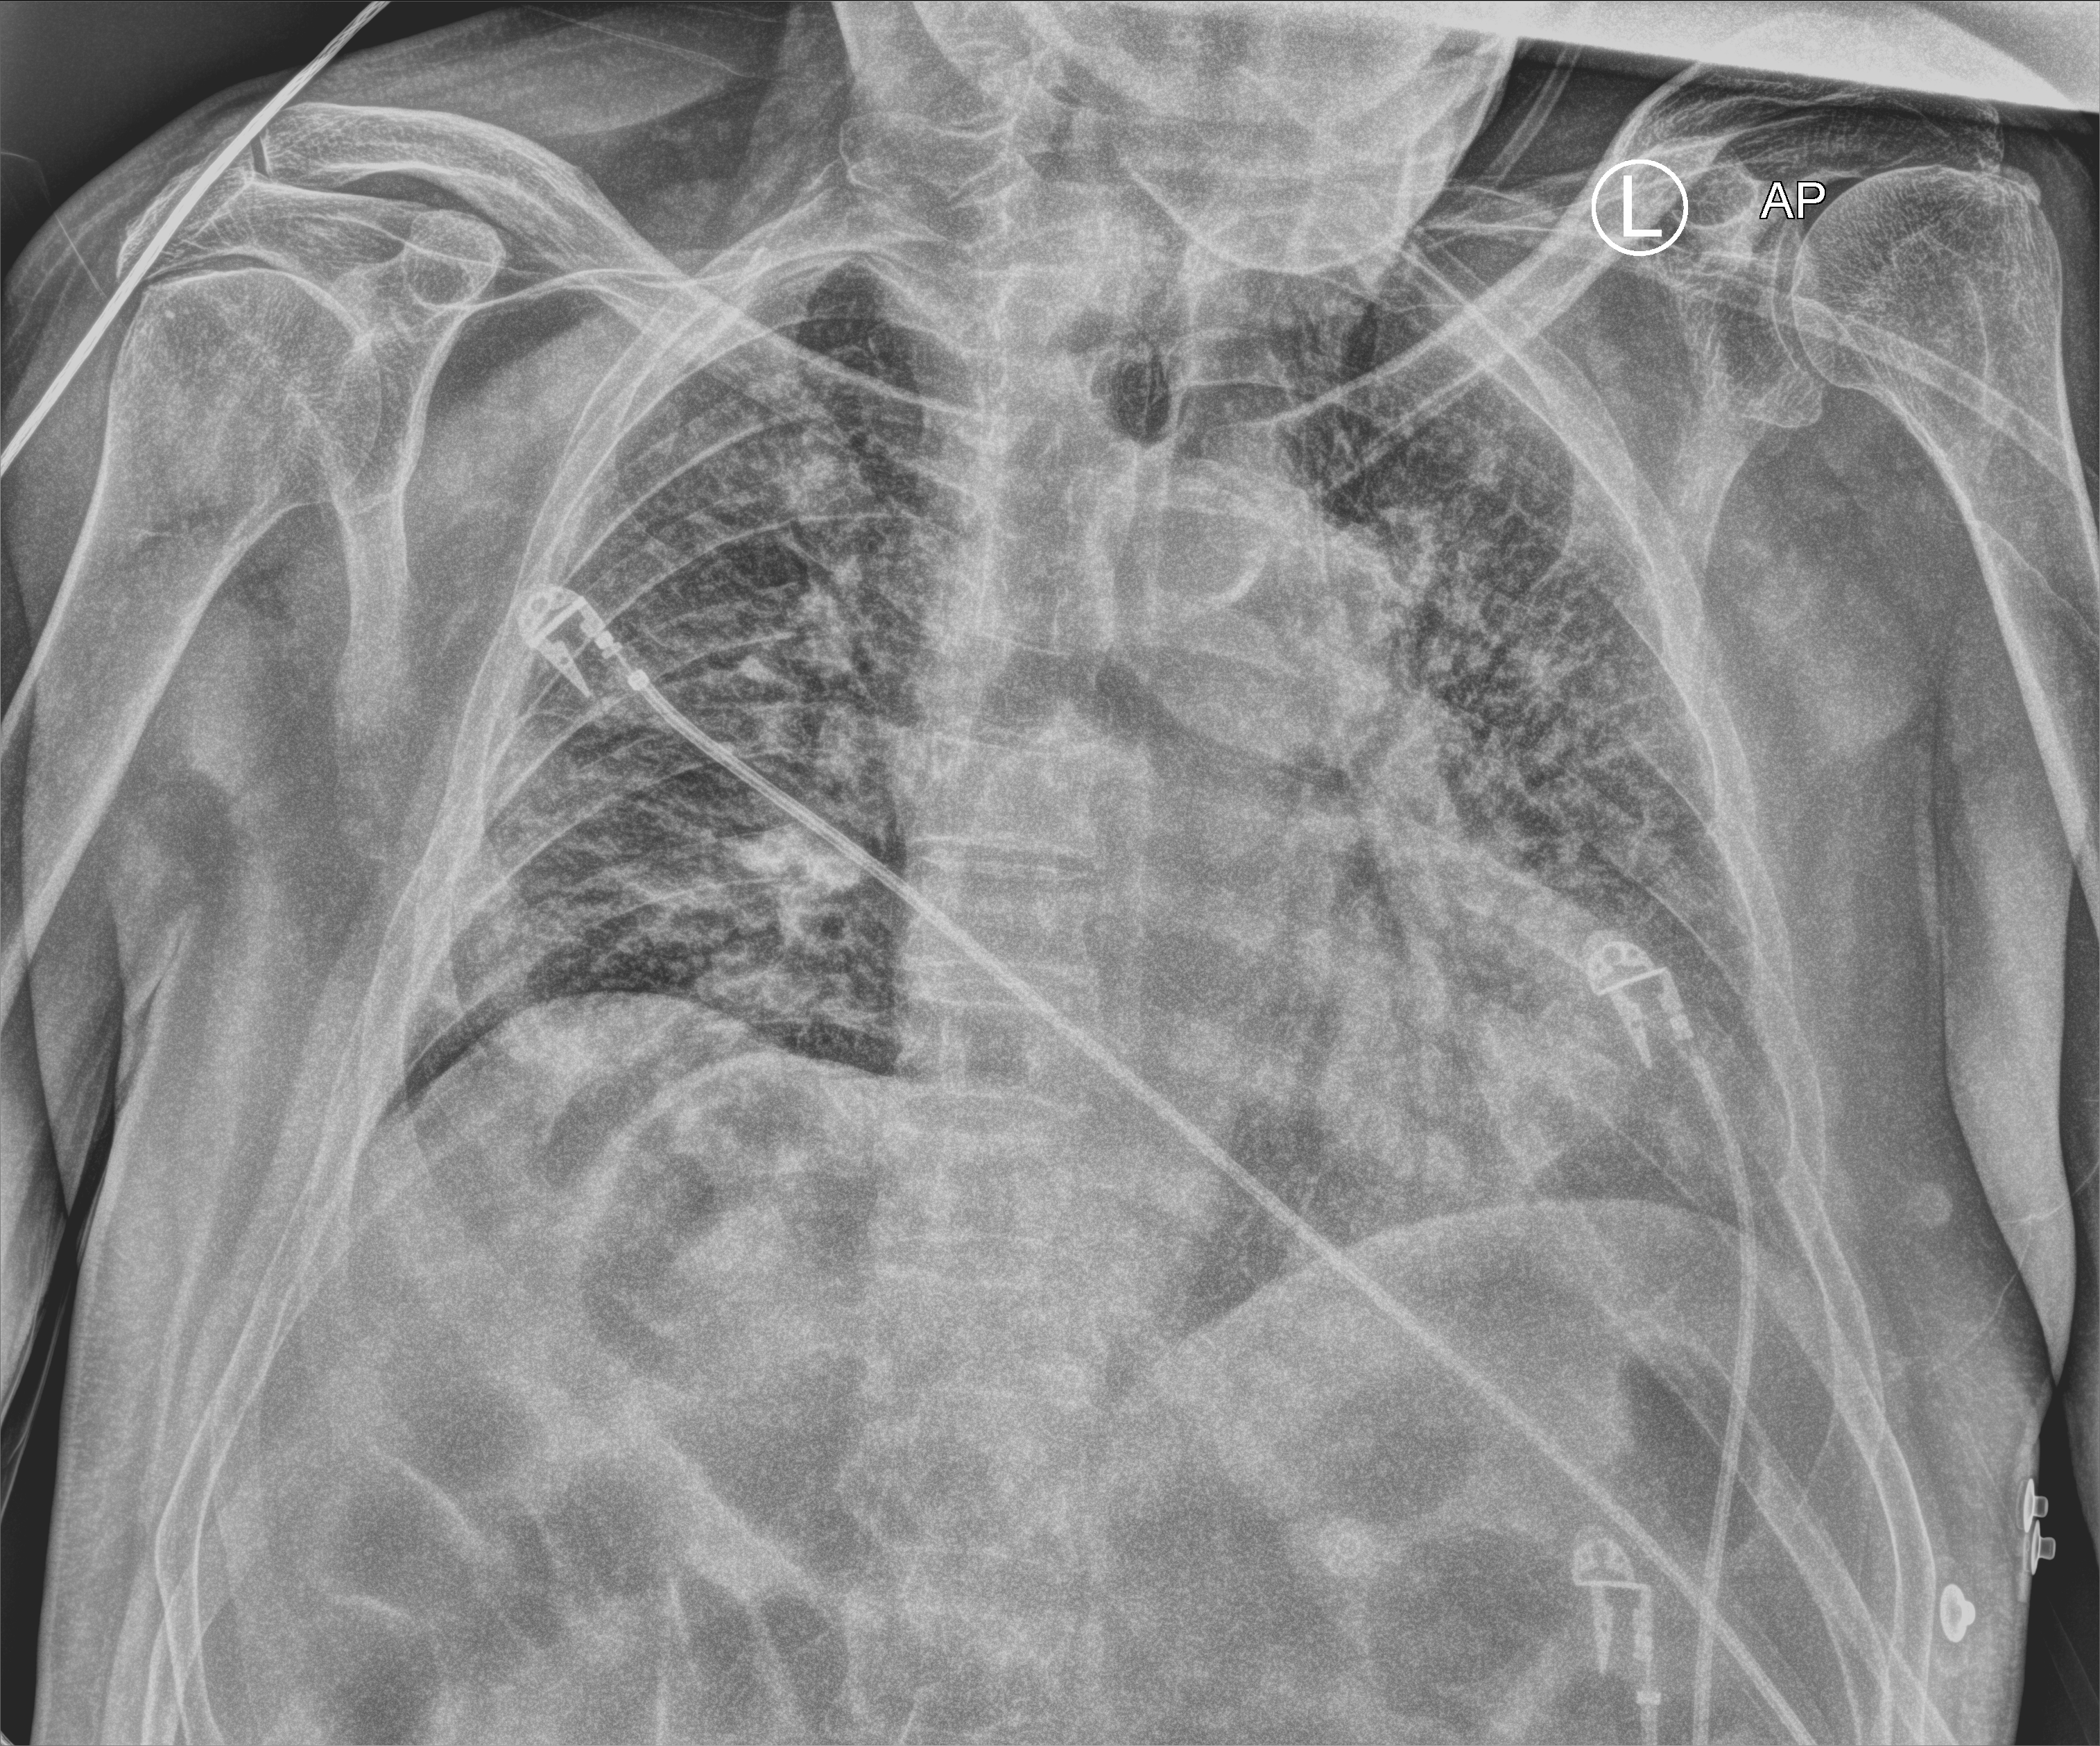
Chest X-ray (portable); anteroposterior (AP) projection. Patient hospitalised with COVID-19; male, aged 60–74 years.
Hospital-stay facts (about this admission, not read from this image; timing relative to this image not recorded): admitted to intensive care during this hospital stay: yes.